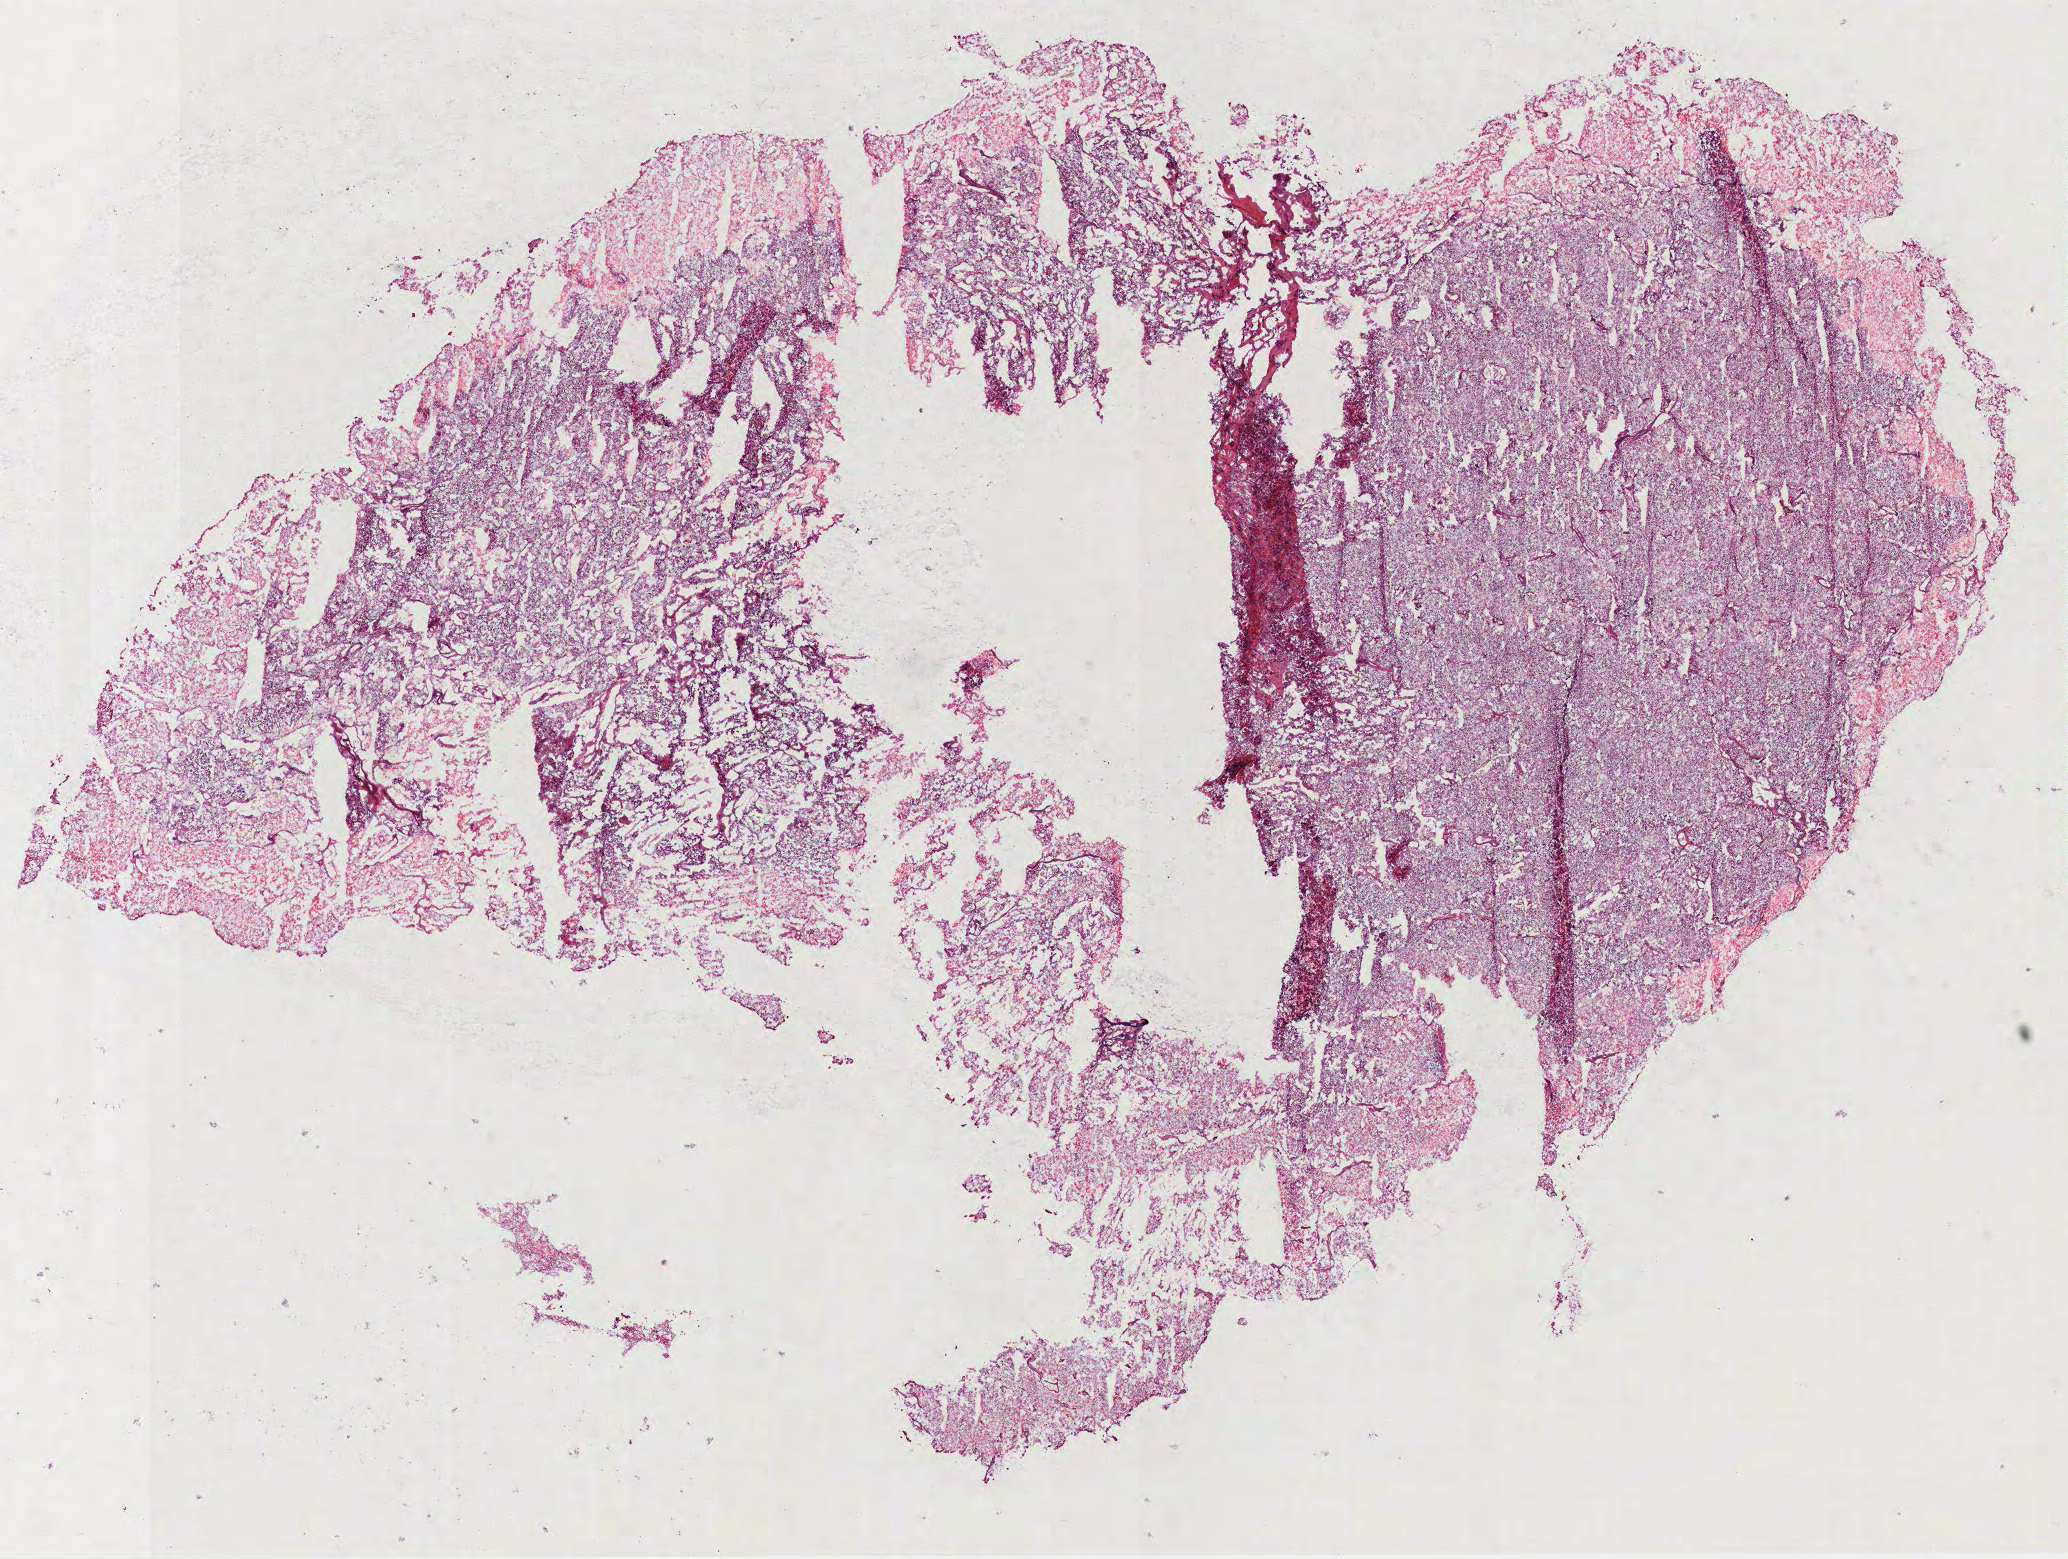
Whole-slide histology image, H&E, whole scanned area (about 16.7 x 12.6 mm) shown as a low-resolution overview. Frozen section from the bottom of the tissue portion. Sample: primary tumour, kidney. Female patient; age at initial diagnosis 42 years. Composition of this section per pathologist review: tumour cells 100%, tumour nuclei 90%, normal cells 0%, stromal cells 0%, necrosis 0%. Infiltration values recorded for this section: lymphocyte infiltration 0%, monocyte infiltration 0%, neutrophil infiltration 0%.
* AJCC pathologic stage: I (6th edition)
* TNM: T1b N0
* pathologic diagnosis: Renal cell carcinoma, chromophobe type